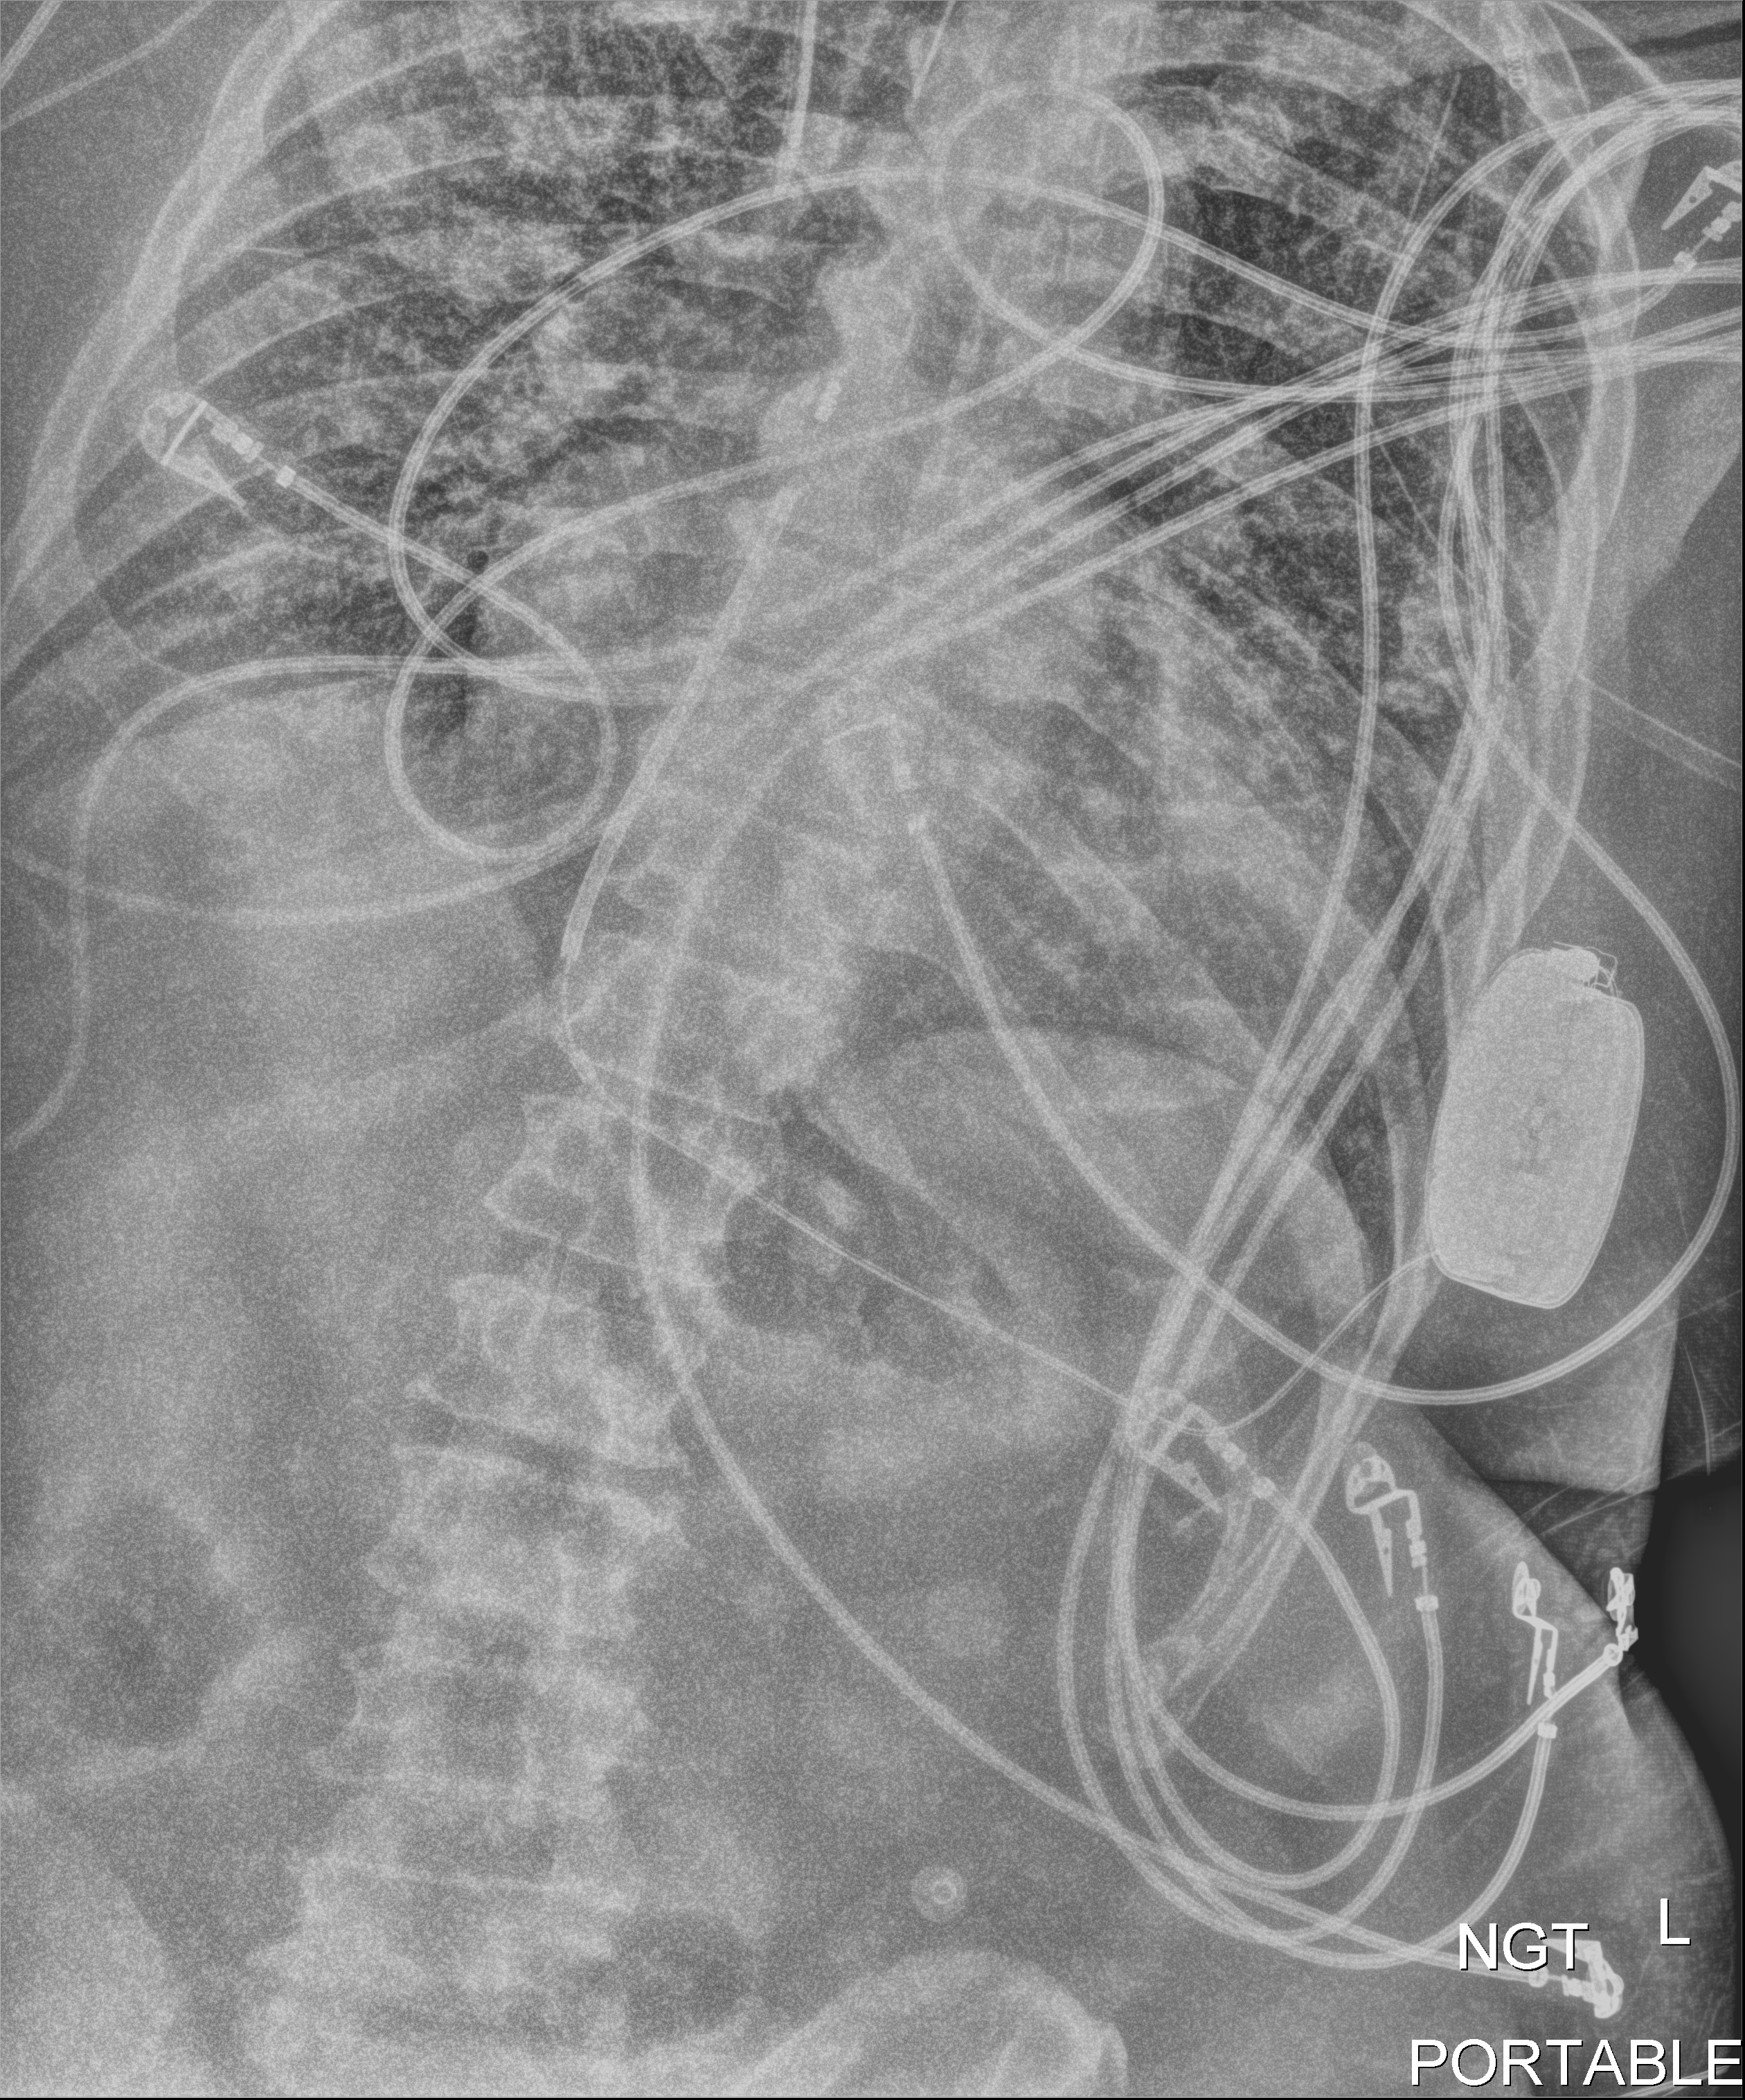
Bedside chest radiograph (digital radiography); anteroposterior (AP) projection. Male patient hospitalised with COVID-19, age 60–74 years.
Hospital-stay facts (about this admission, not read from this image; timing relative to this image not recorded):
- mechanically ventilated during this hospital stay: yes